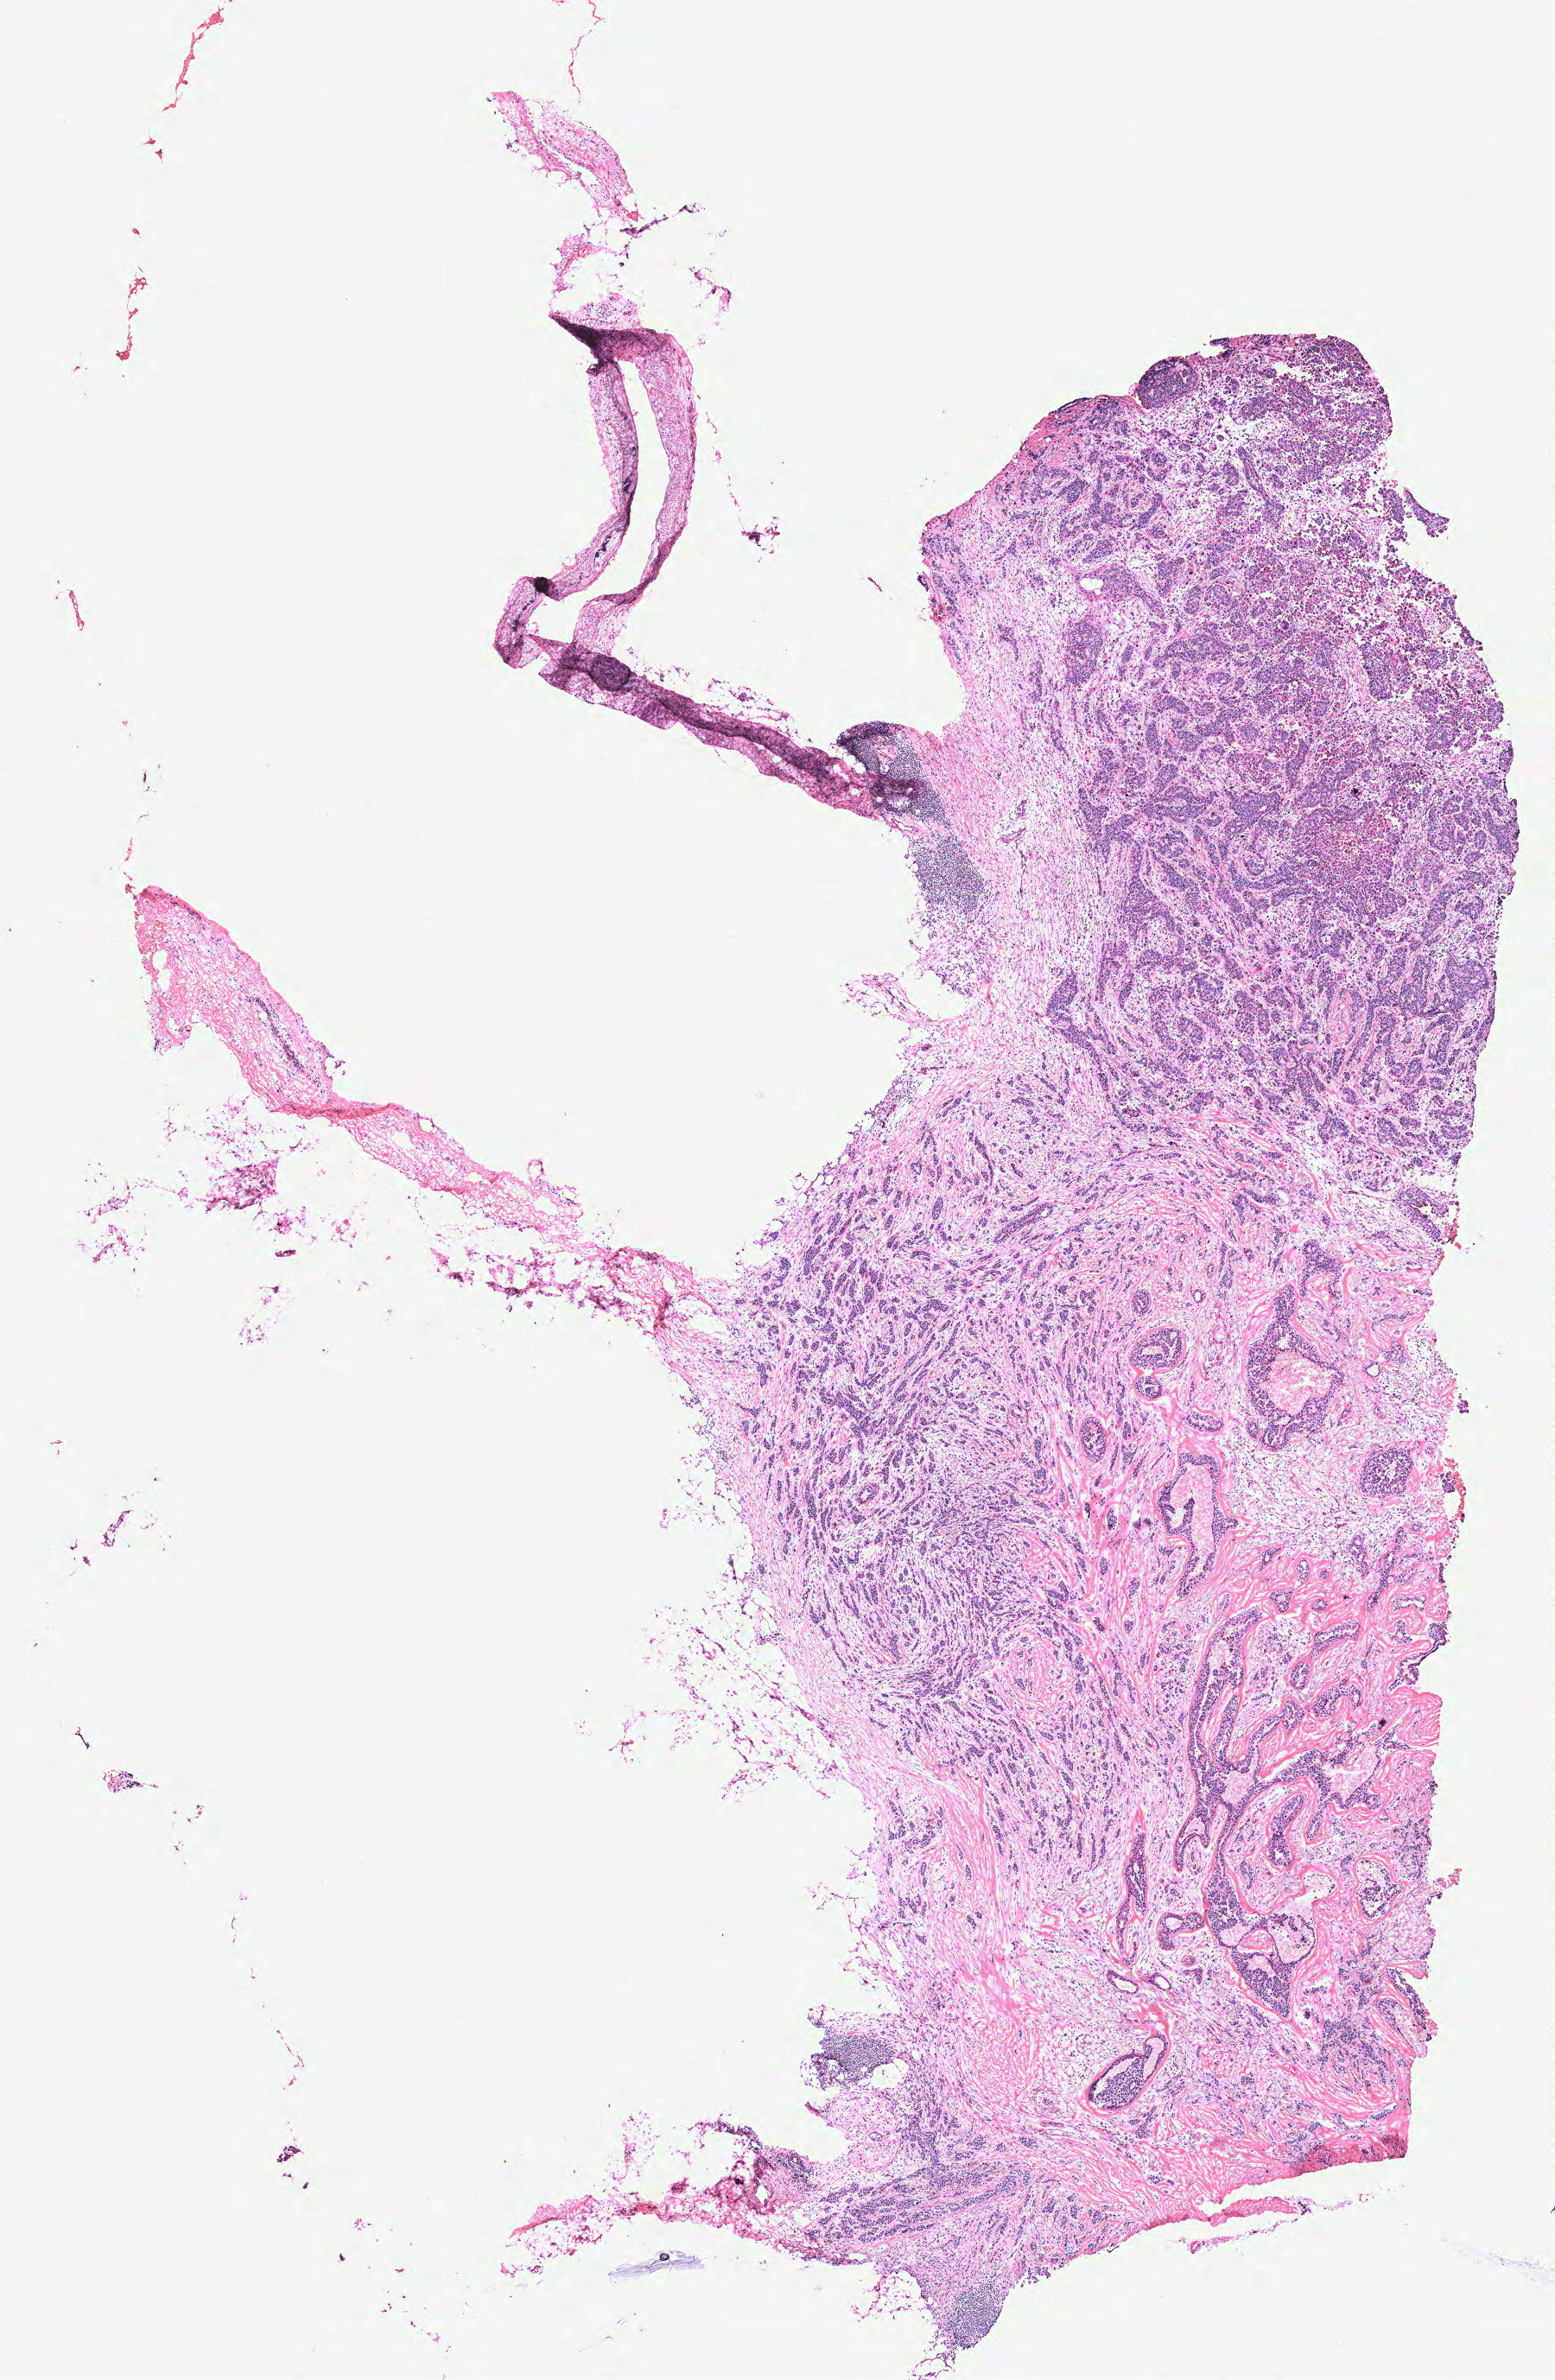
Whole-slide histology image, H&E-stained, low-resolution overview of the scanned area, about 7.2 x 11.0 mm (acquisition: 40x scan), breast, tissue type not recorded. Patient: female, age 59 years.
• patient diagnosis: Infiltrating duct carcinoma, NOS